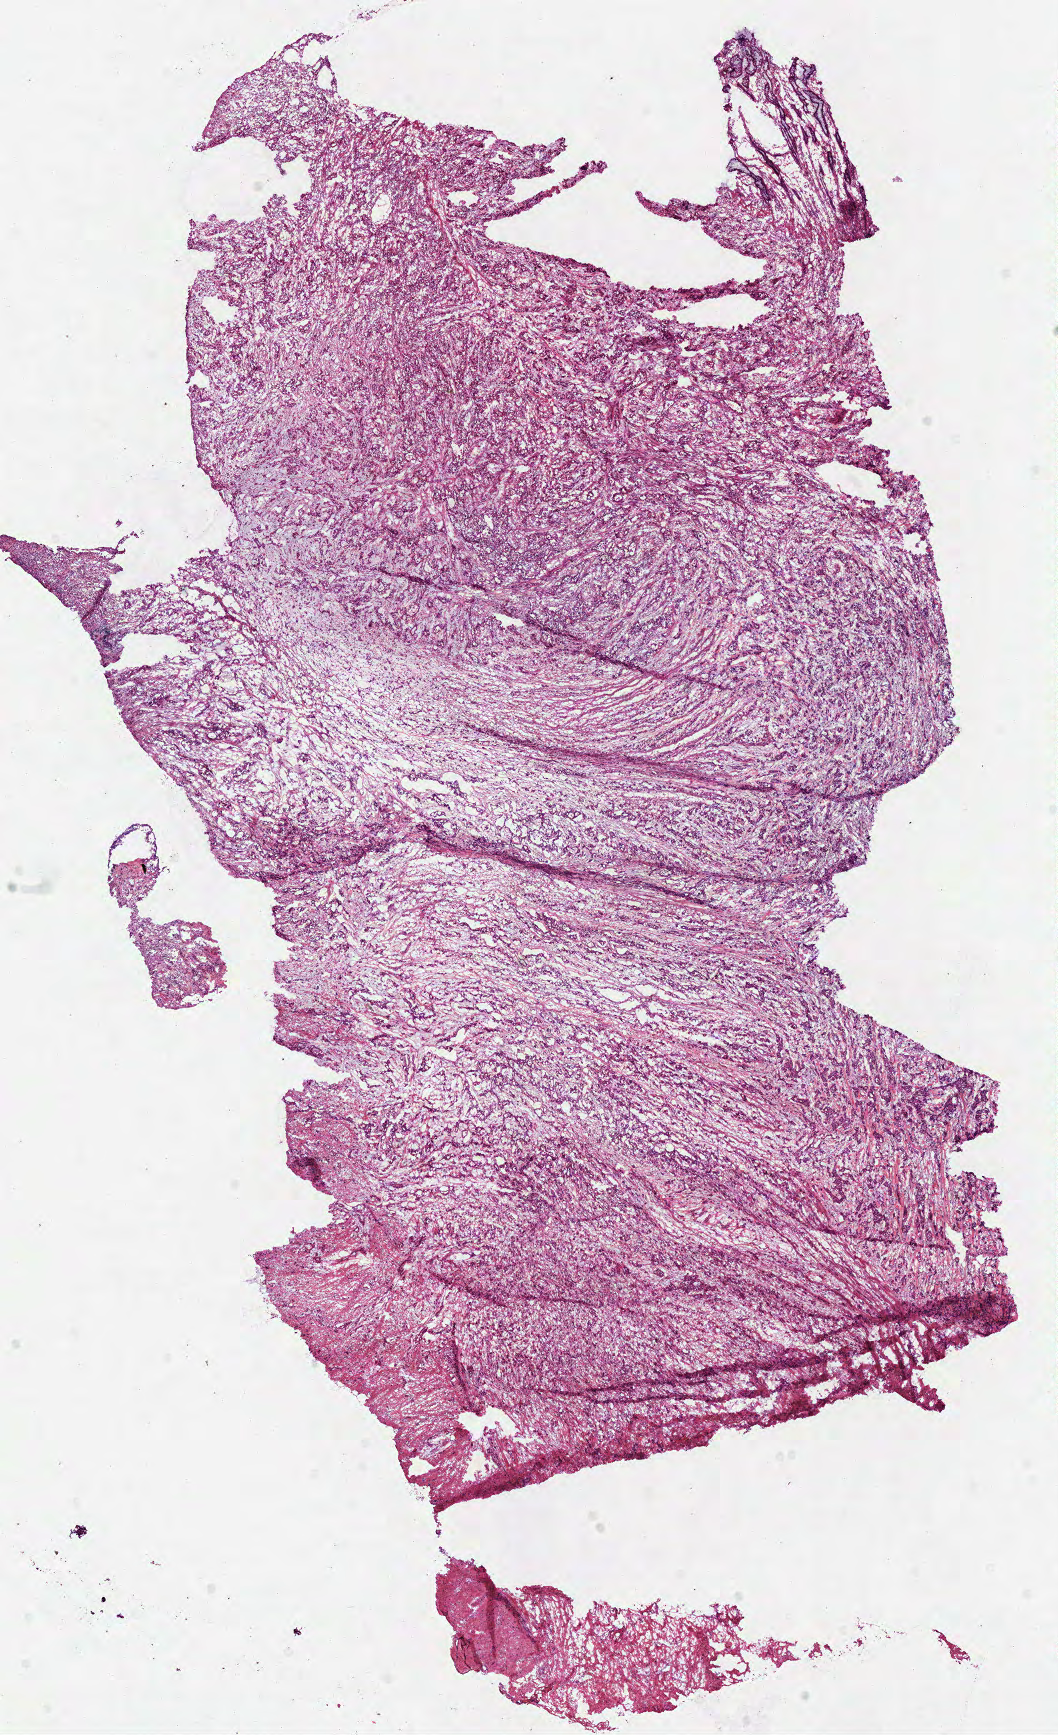
Digitized H&E-stained tissue section (whole slide), whole scanned area (about 8.3 x 13.6 mm) shown as a low-resolution overview, frozen section, colon, primary tumour sample. Male, age 69 years at initial diagnosis. Slide review estimates, as recorded: tumour cells 80%, tumour nuclei 80%, normal cells 0%, stromal cells 20%, necrosis 0%.
* lymph nodes positive (case pathology): 5 of 19 examined
* AJCC pathologic stage: IV (6th edition)
* diagnosis: Adenocarcinoma, NOS (sigmoid colon)